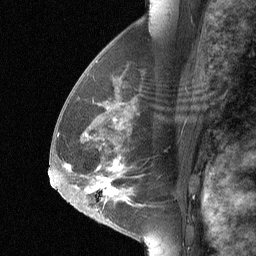
Breast MRI (dynamic contrast-enhanced), one sagittal slice. Slice 35 of 64 in the series (ordered by position). Dynamic contrast-enhanced study with each time point stored as its own series, time point 2 of 3 at this slice position (early post-contrast, ordered by acquisition time). 1.5 T. TE 4.8 ms, TR 27 ms. 2 mm slice thickness. 256 × 256 image matrix, field of view 180 × 180 mm. Female patient, age 56 years. From the clinical record (not read from this slice): setting: breast cancer imaged before/during neoadjuvant chemotherapy; receptor status: HER2-positive.
Structures marked on this image (semi-automatically segmented with operator editing):
- analysis volume of interest (the breast-tissue region the enhancement analysis was run in; not a lesion): bounding box [x1, y1, x2, y2] px = [68, 83, 155, 214]
- tumour enhancement mask (voxels above the 90 % enhancement threshold inside the analysis volume of interest): [86, 162, 119, 195]